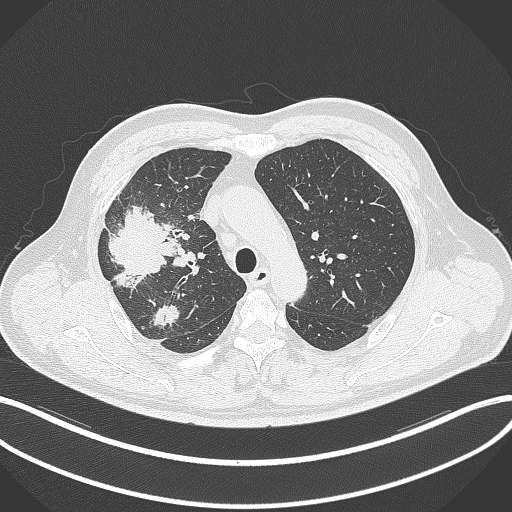
Chest CT, one axial slice. Slice 242 of 348 in the series (ordered by position). Lung window (W 1500 / L -600 HU). 1 mm slice thickness. 512 × 512 image matrix. Male patient, age 55 years. Case-level facts recorded for this patient, not image findings: clinical TNM (as recorded): T3 N2 M1.
Outlined on this slice (rectangle marked by the reading radiologist):
- lung tumour (recorded histology: adenocarcinoma): bounding box (x1, y1, x2, y2) in pixels: (103, 203, 181, 289)